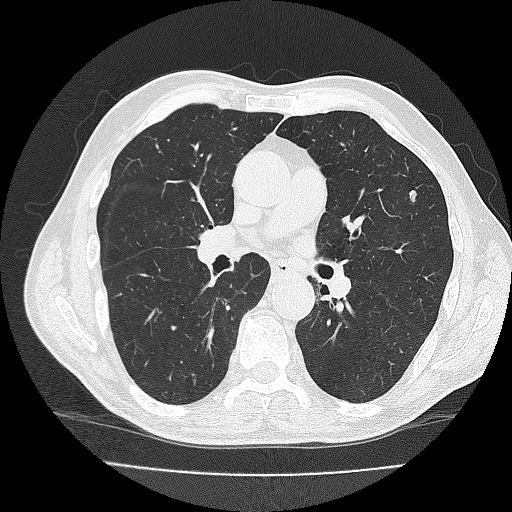
Axial slice from a low-dose chest CT screening exam, second screening round (one year after baseline), lung window (W 1500 / L -600 HU), 2 mm slice thickness, reconstruction kernel FC30 (as recorded), slice 97 of 206 in the series. Male, age 71 years at enrolment.
- Expert-annotated lung lesion, box from (x=387, y=178) to (x=428, y=223) px.
- Screening reader's record for this exam: no non-calcified nodule ≥4 mm recorded.
- Official screen result: negative screen, minor abnormalities not suspicious for lung cancer.
- Participant outcome: lung cancer diagnosed 387 days after this screen — adenocarcinoma, NOS, left upper lobe, moderately differentiated (G2), stage IA (AJCC 6th edition), 10 mm at pathology.